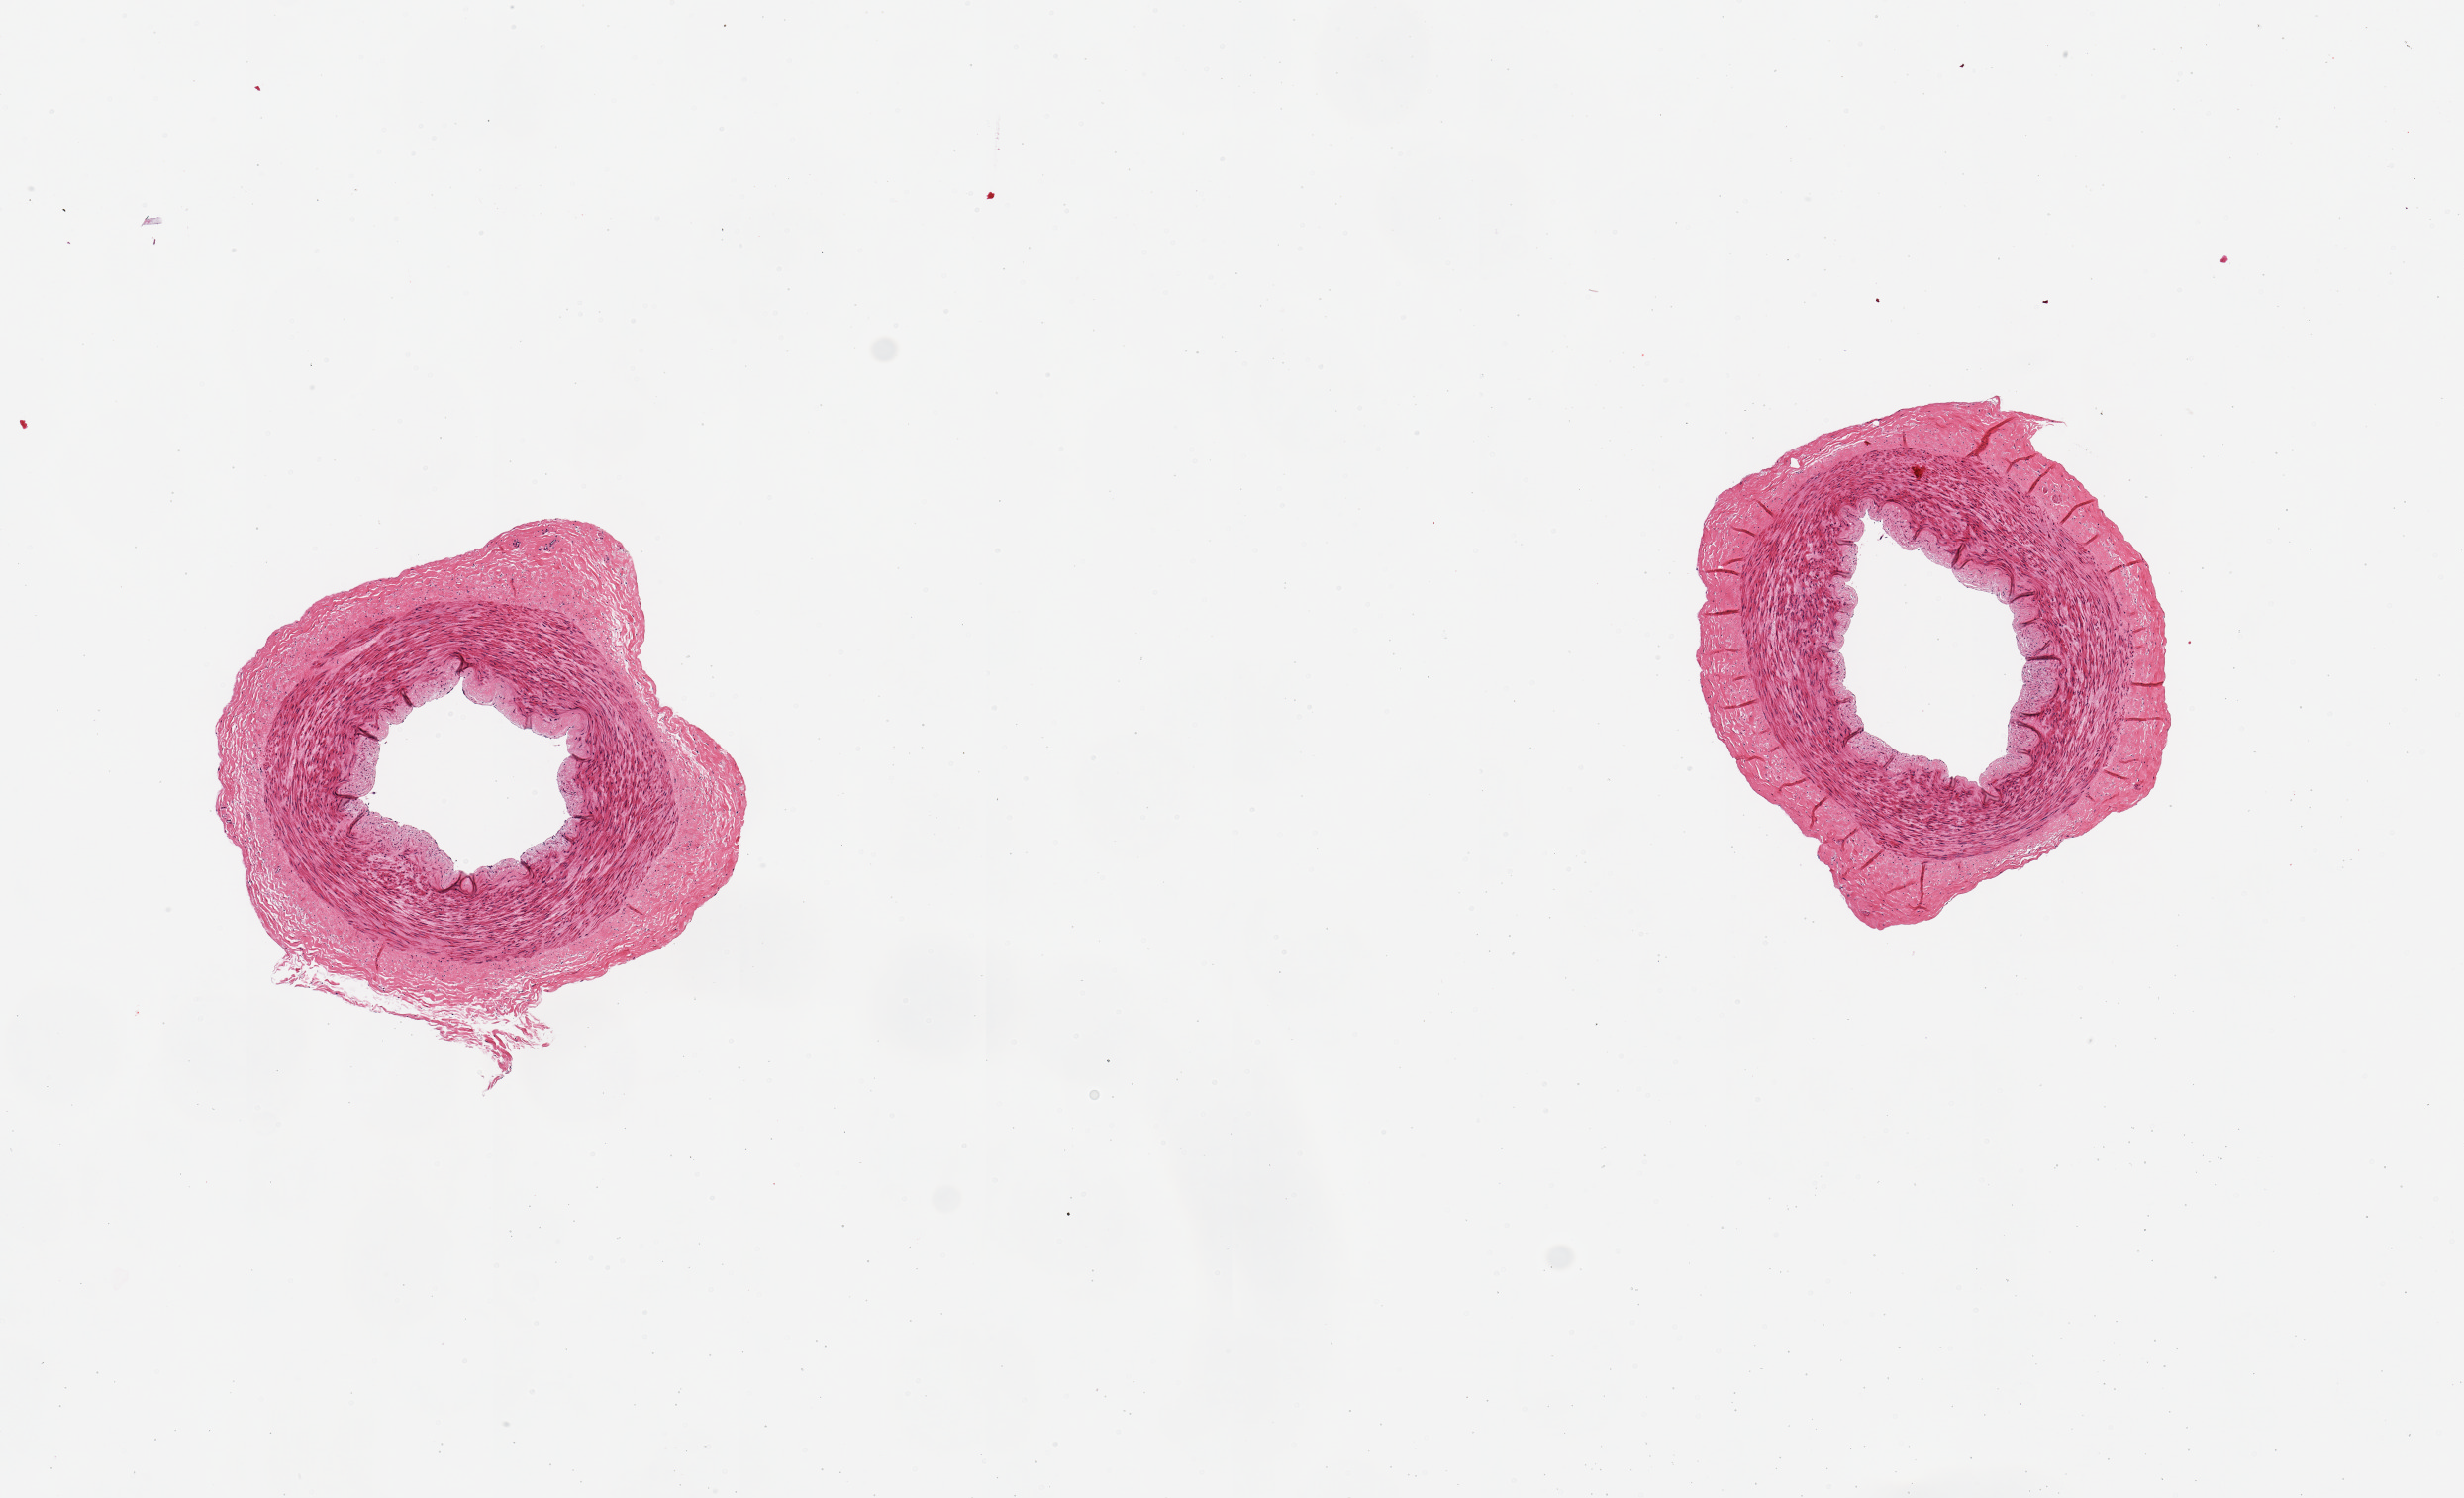
Whole-slide image, haematoxylin and eosin stain — a low-resolution overview of the entire scanned area, about 9.8 x 6.0 mm (slide scanned at 20x), PAXgene-fixed paraffin-embedded (PFPE) section, target tissue: tibial artery, tissue donor sample. Male donor.
Reviewer comment on this tissue sample: 2 pieces, 2x2 & 2x2mm; good clean specimen; no fat.